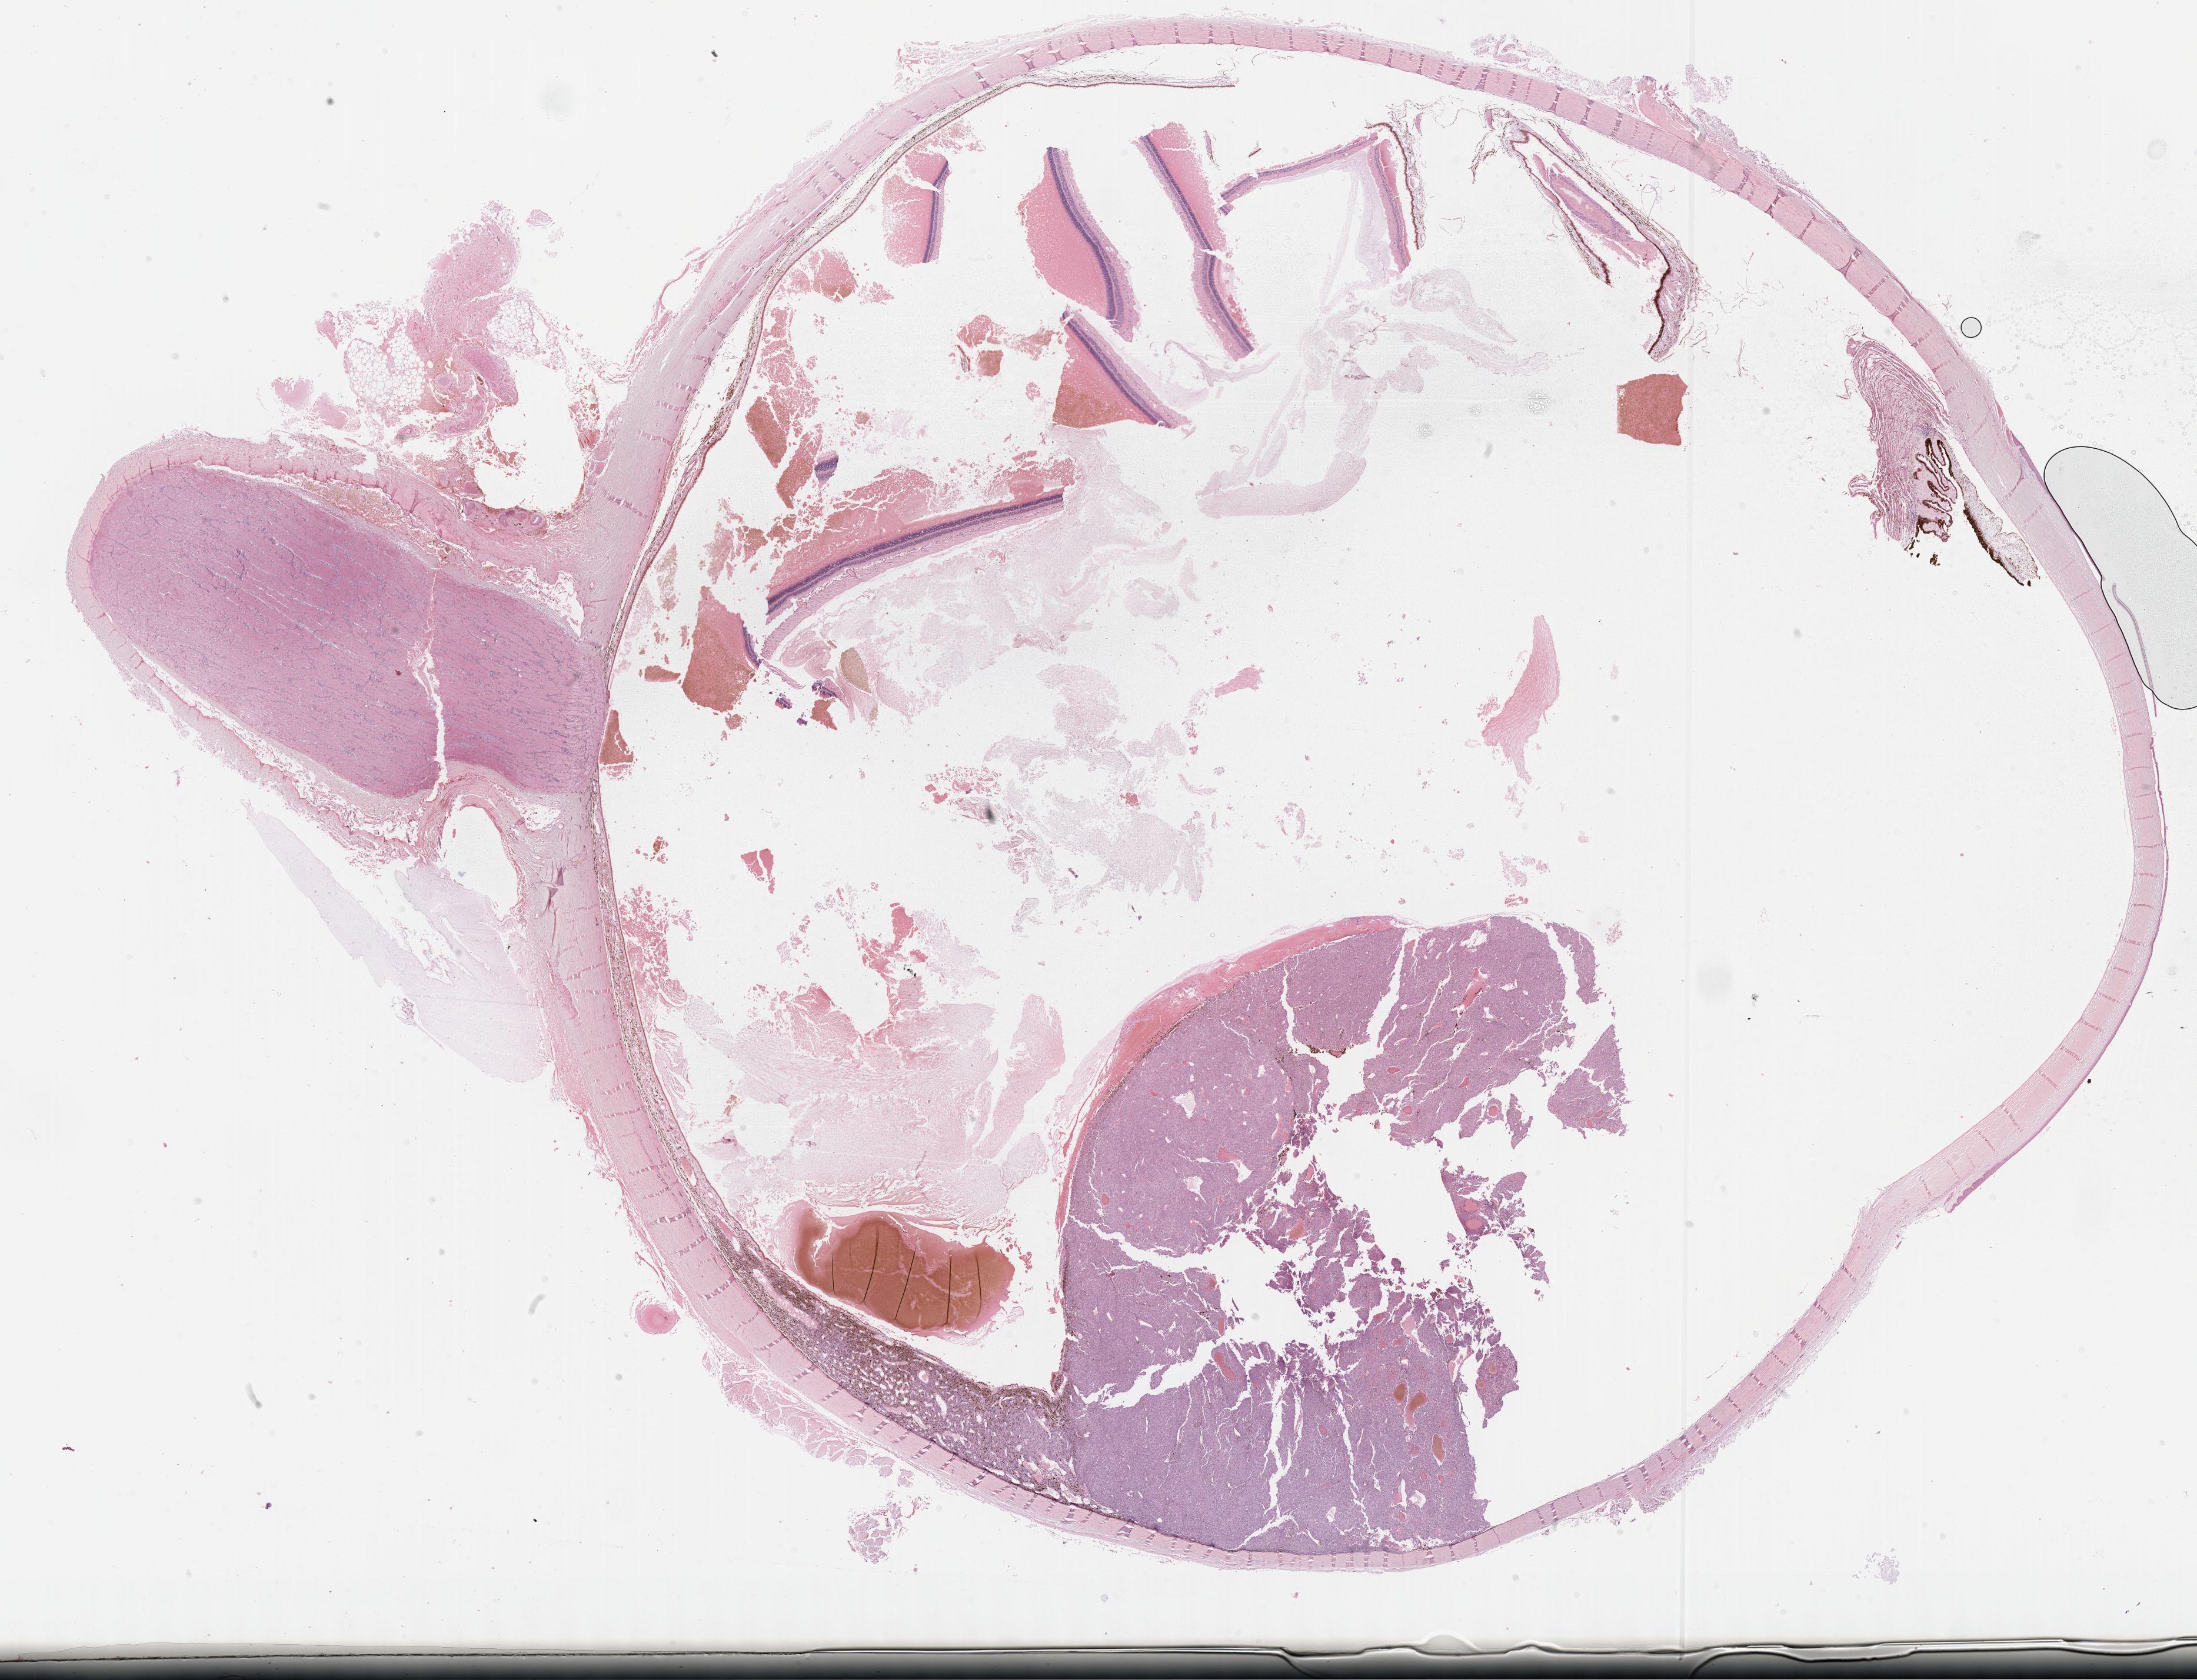
Digitized H&E-stained tissue section (whole slide) — shown as a low-resolution overview of the whole scanned area (about 30.2 x 23.1 mm), formalin-fixed paraffin-embedded (FFPE) diagnostic section, sample: primary tumour, uvea. Patient: female, age at initial diagnosis 44 years.
Diagnosis: Mixed epithelioid and spindle cell melanoma (choroid).